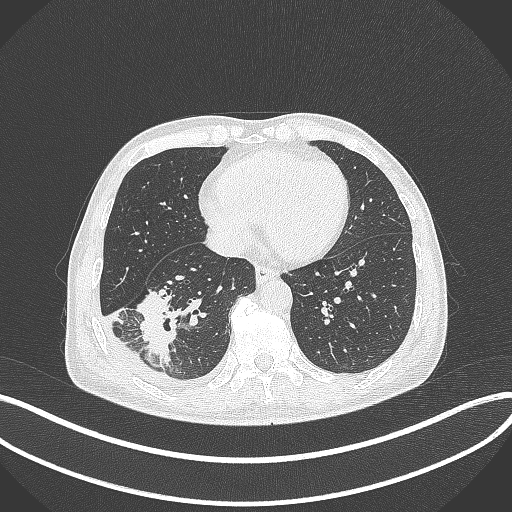
Chest CT, one axial slice. Position 127 of 388 along the scan axis. Lung window (W 1500 / L -600 HU). 1 mm slice thickness. 512 × 512 image matrix. Patient: male, 64 years. From the clinical record (not read from this slice): clinical TNM (as recorded): T3 N0 M0; histopathological grade: G2-3.
Outlined on this slice (bounding box drawn by a radiologist):
- lung tumour (recorded histology: adenocarcinoma): bounding box [x1, y1, x2, y2] px = [137, 289, 184, 374]